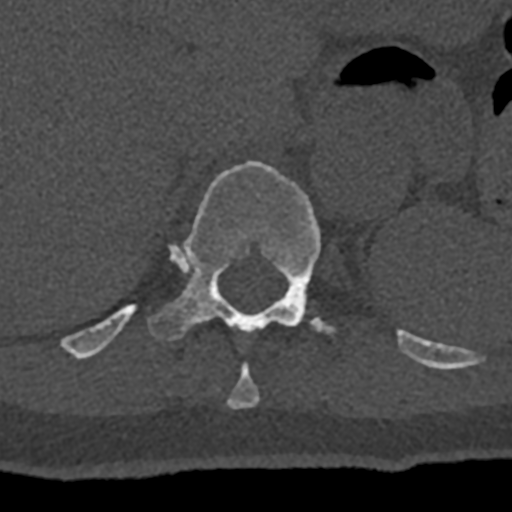
CT including the spine, one axial slice; position 551 of 797 along the scan axis; bone window (W 1800 / L 400 HU); 0.5 mm slice thickness; 512 × 512 image matrix, field of view 160 × 160 mm. Male patient, age 74 years. Case-level facts recorded for this patient, not image findings: primary cancer: renal; vertebrae with lytic lesions (as recorded): T10, L1, L2, L3, L4, L5.
Outlined on this slice (semi-automatic segmentation, software-assisted and operator-edited):
- T10 vertebra: bounding box <227,363,260,409> (left, top, right, bottom; pixels)
- T11 vertebra: <70,161,432,367>